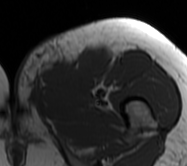
MRI of an extremity soft-tissue mass, one axial slice; position 18 of 62 along the scan axis; MR volume resampled by the dataset authors to the PET/CT grid (not the native acquisition matrix); 187 × 166 image matrix, field of view 183 × 162 mm. Female patient. From the clinical record (not read from this slice): histological type: leiomyosarcoma; grade: high; site of the primary tumour: groin.
Annotated regions visible in this slice (expert contour drawn on MRI and transferred to this co-registered scan by the dataset authors):
- gross tumour volume including surrounding oedema: bounding box (x1, y1, x2, y2) in pixels: (14, 40, 110, 116)
- gross tumour volume (mass): (39, 51, 110, 93)